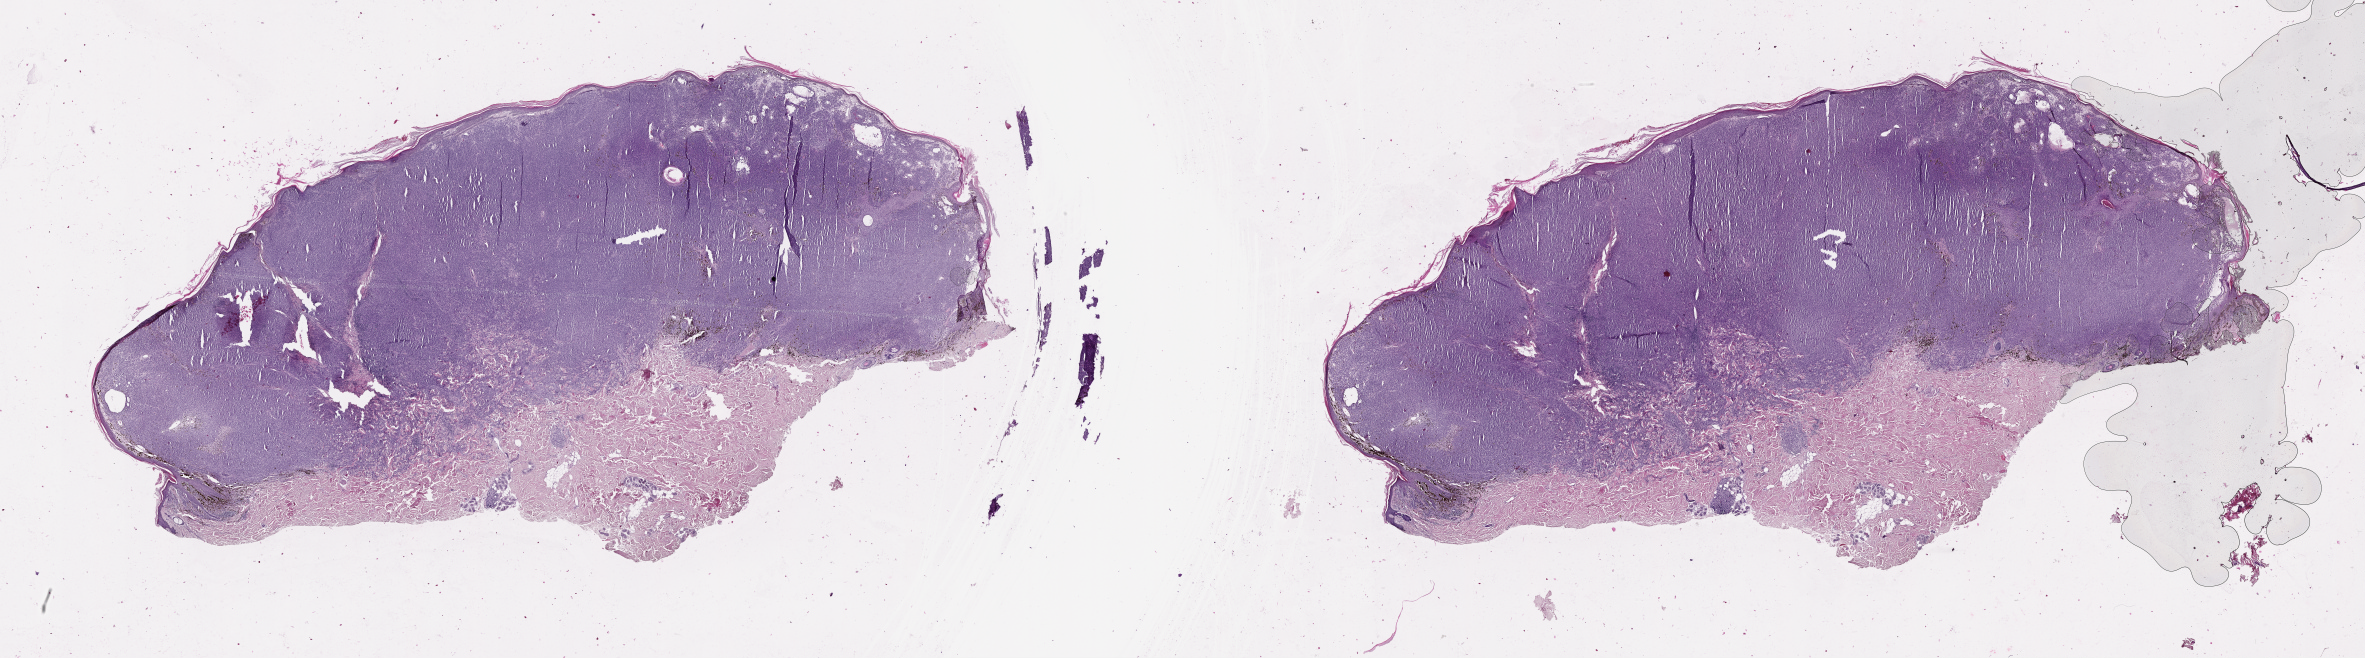
Whole-slide histology image, H&E, whole scanned area (about 38.1 x 10.6 mm, acquisition: 20x scan) shown as a low-resolution overview. Patient: female, age 74 years.
Patient diagnosis: Malignant melanoma, NOS.